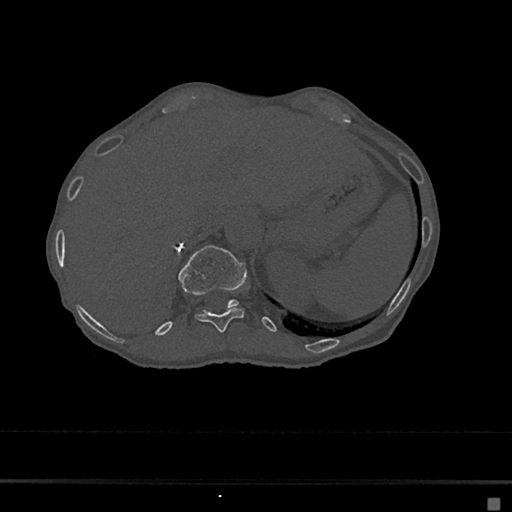
CT including the spine, one axial slice; position 158 of 797 along the scan axis; bone window (W 1800 / L 400 HU); 0.5 mm slice thickness; 512 × 512 image matrix, field of view 360 × 360 mm. Patient: female, 68 years. Case-level facts recorded for this patient, not image findings: primary cancer: renal.
Structures marked on this image (semi-automatically segmented with operator editing):
- T11 vertebra: bounding box [x1, y1, x2, y2] px = [196, 308, 245, 332]
- T12 vertebra: [178, 245, 247, 308]